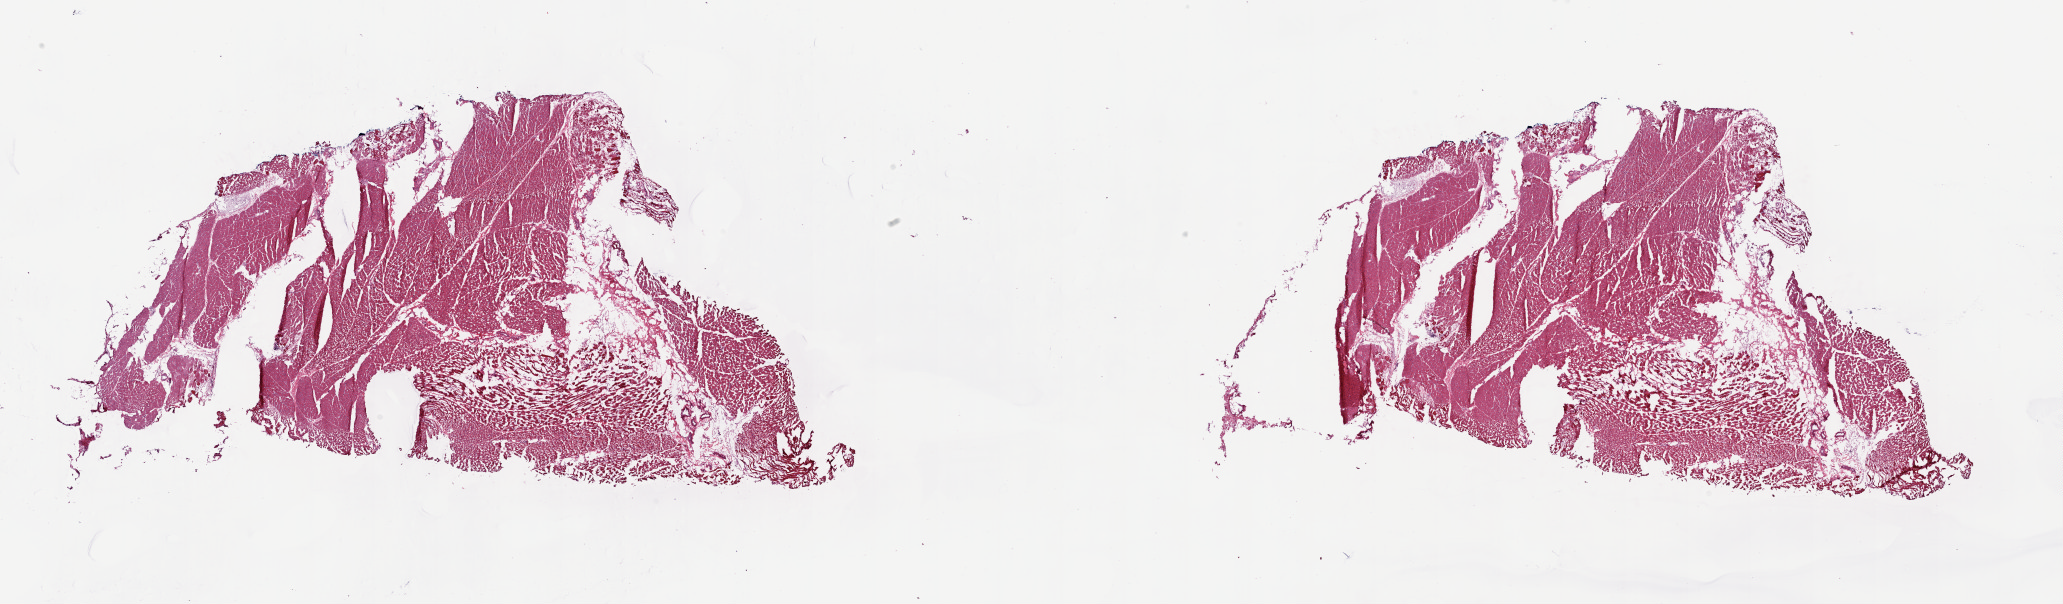
Hematoxylin and eosin (H&E) stained whole-slide image — a low-resolution overview of the entire scanned area, about 32.7 x 9.6 mm (slide scanned at 20x); frozen section from the top of the tissue portion; solid tissue normal (non-tumour tissue) sample from the connective, subcutaneous and other soft tissues. Male, age 66 years at initial diagnosis. Slide review estimates, as recorded: tumour cells 0%, tumour nuclei 0%, normal cells 0%, stromal cells 100%, necrosis 0%. Infiltration values recorded for this section: lymphocyte infiltration 2%, monocyte infiltration 1%, neutrophil infiltration 1%.
- this section: solid tissue normal sample (biorepository sample class)
- patient diagnosis: Undifferentiated sarcoma (connective, subcutaneous and other soft tissues of pelvis)